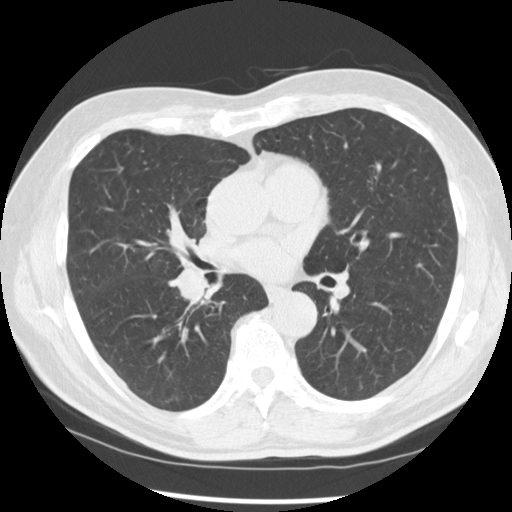
Low-dose screening chest CT, axial slice, first (baseline) screen, lung window (W 1500 / L -600 HU), 2.5 mm slice thickness, slice 147 of 277 in the series, 512 × 512 image matrix, field of view 365 × 365 mm. Male participant, aged 67 years at enrolment. Current smoker at enrolment.
Expert reader's lesion annotation, box from (x=158, y=247) to (x=228, y=313) px. Reader record for this screening exam (exam-level; its link to the box is not recorded): non-calcified nodule or mass ≥4 mm, left lower lobe, 15 × 15 mm, spiculated (stellate) margins, soft tissue attenuation. Note: the box lies in the patient's right hemithorax on this image, whereas the reader's record names the left lung; they may be different findings. Official screen result: positive, change unspecified: nodule(s) >= 4 mm or enlarging nodule(s), mass(es), or other non-specific abnormalities suspicious for lung cancer.